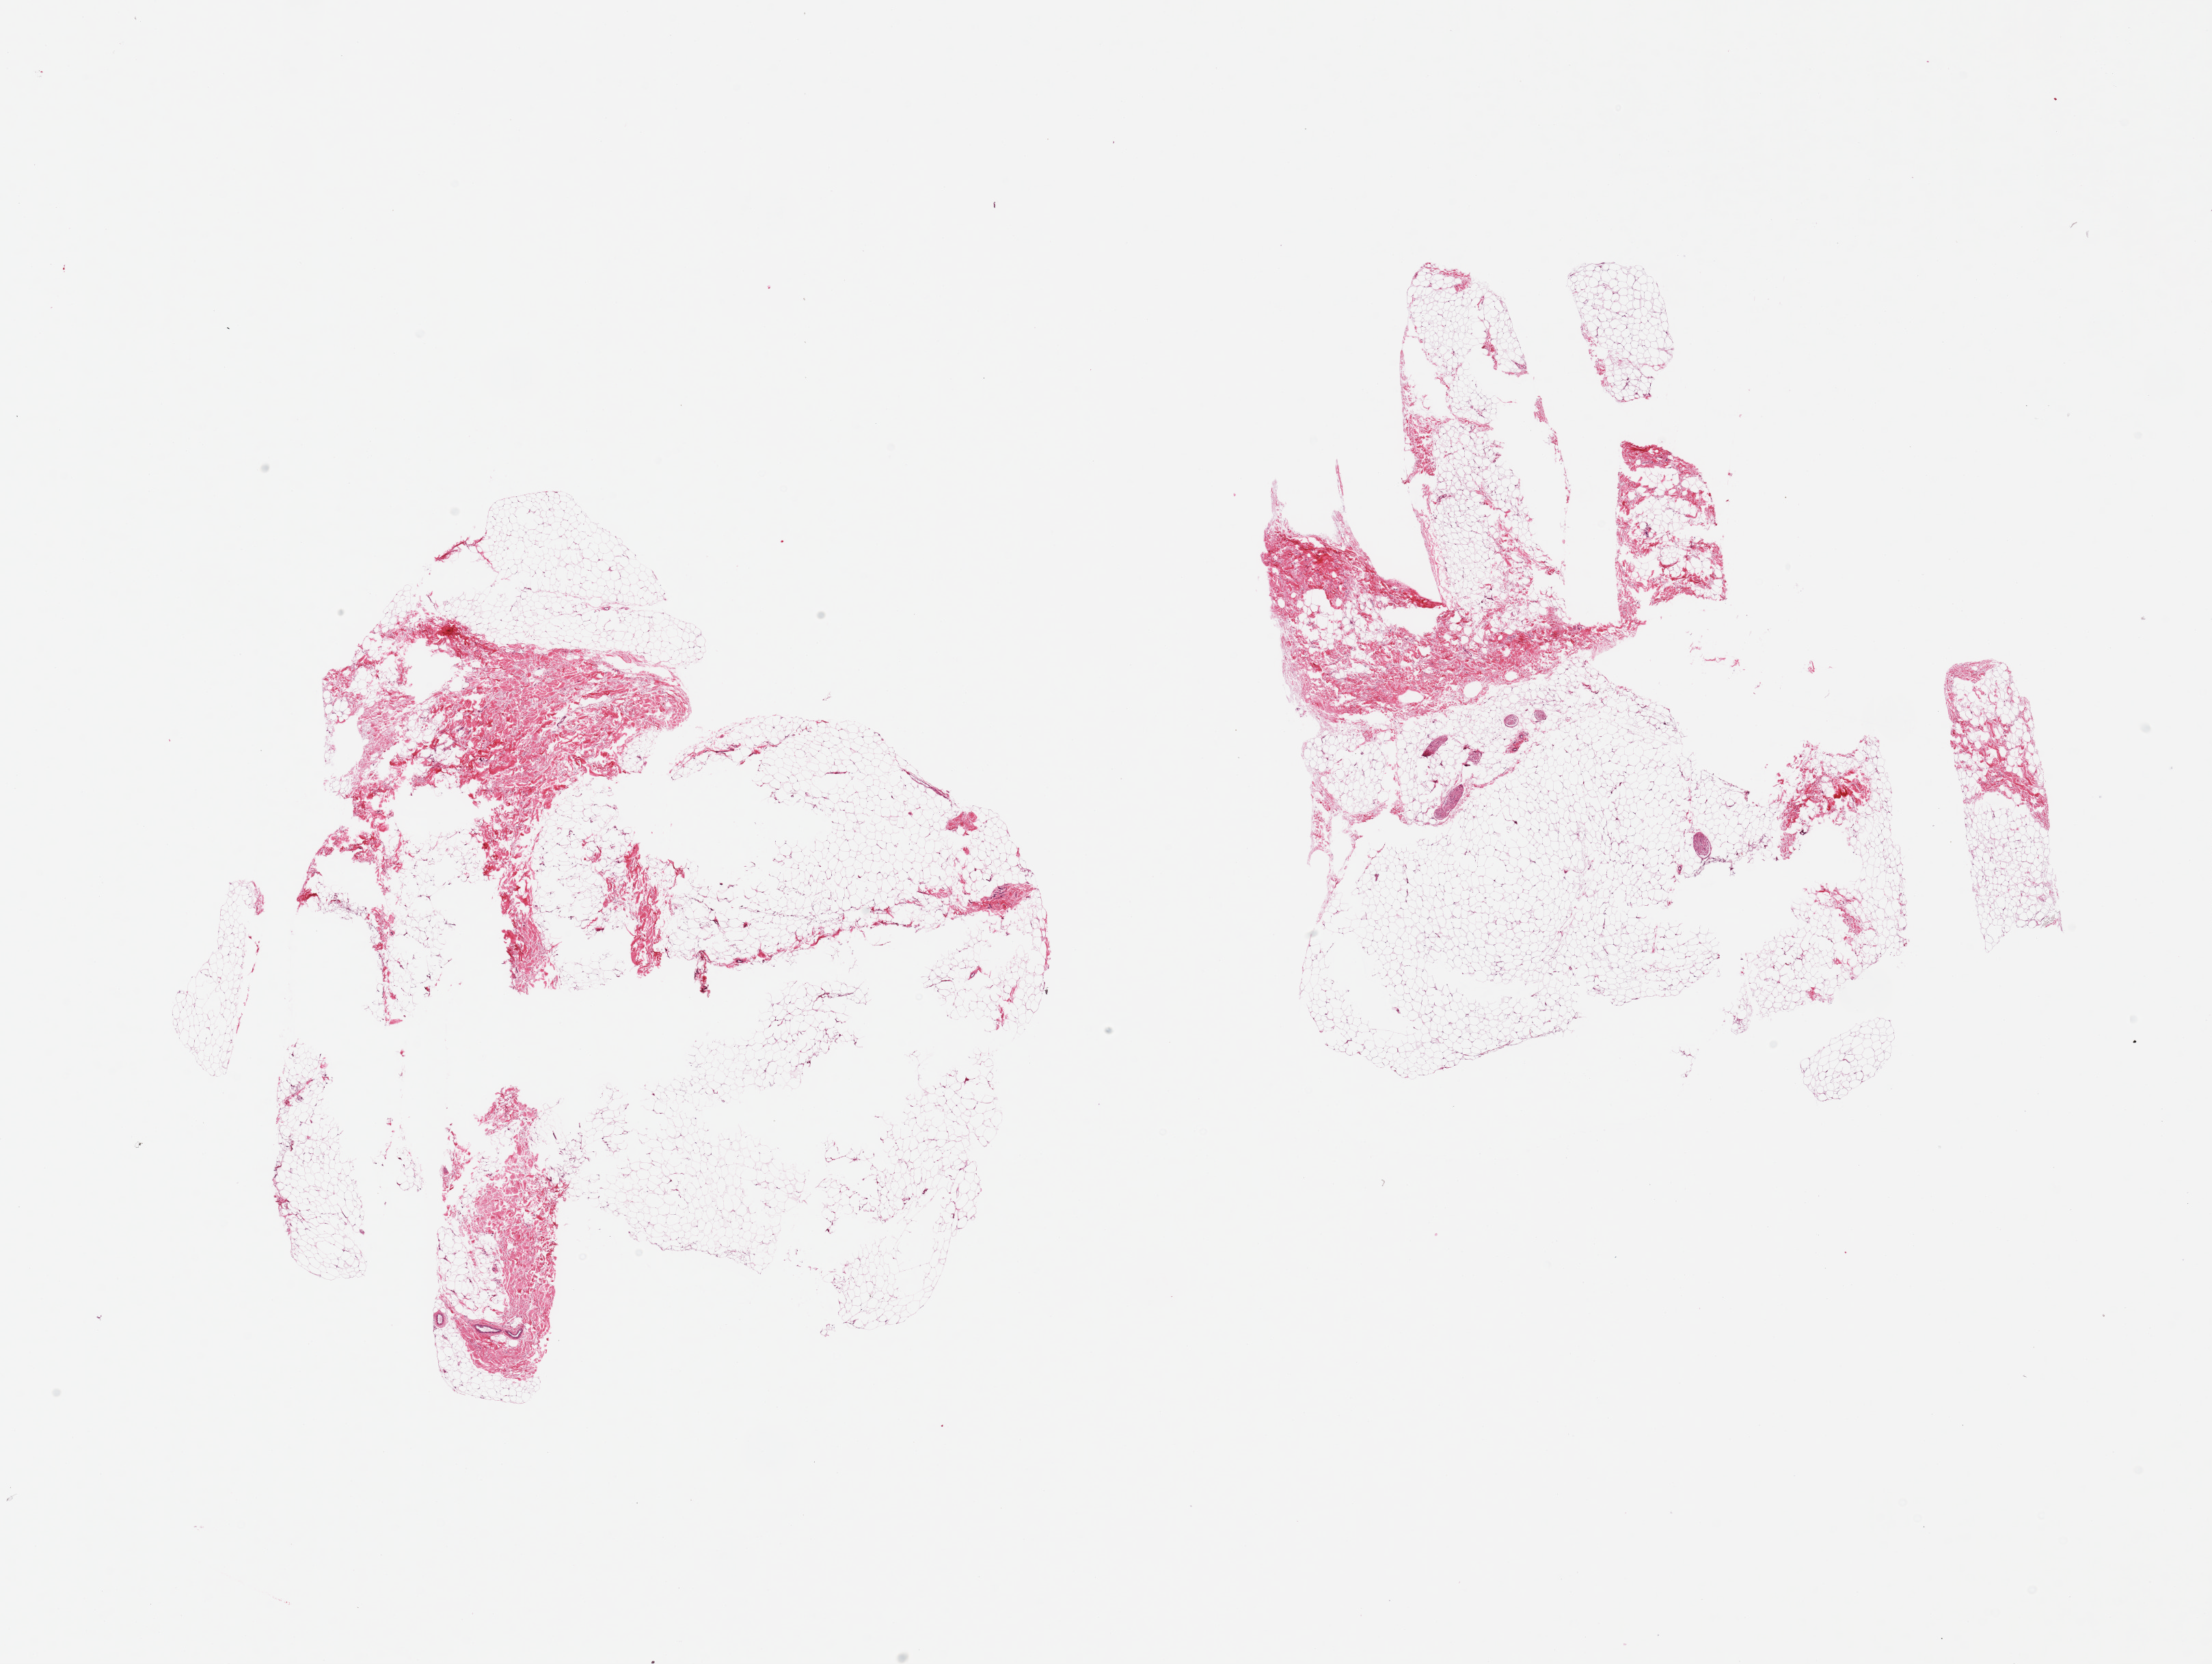
Hematoxylin and eosin (H&E) whole-slide image, brightfield, shown as a low-resolution overview of the whole scanned area (about 25.6 x 19.3 mm, from a 20x scan); PAXgene-fixed, paraffin-embedded tissue; sampled site (target tissue): breast; tissue donor sample. Donor sex: female.
Pathologist's review note for this sample: 2 pieces; 60% mature adipose tissue and 40% fibrovascular tissue and nerves; no definite ducts or lobules identified.